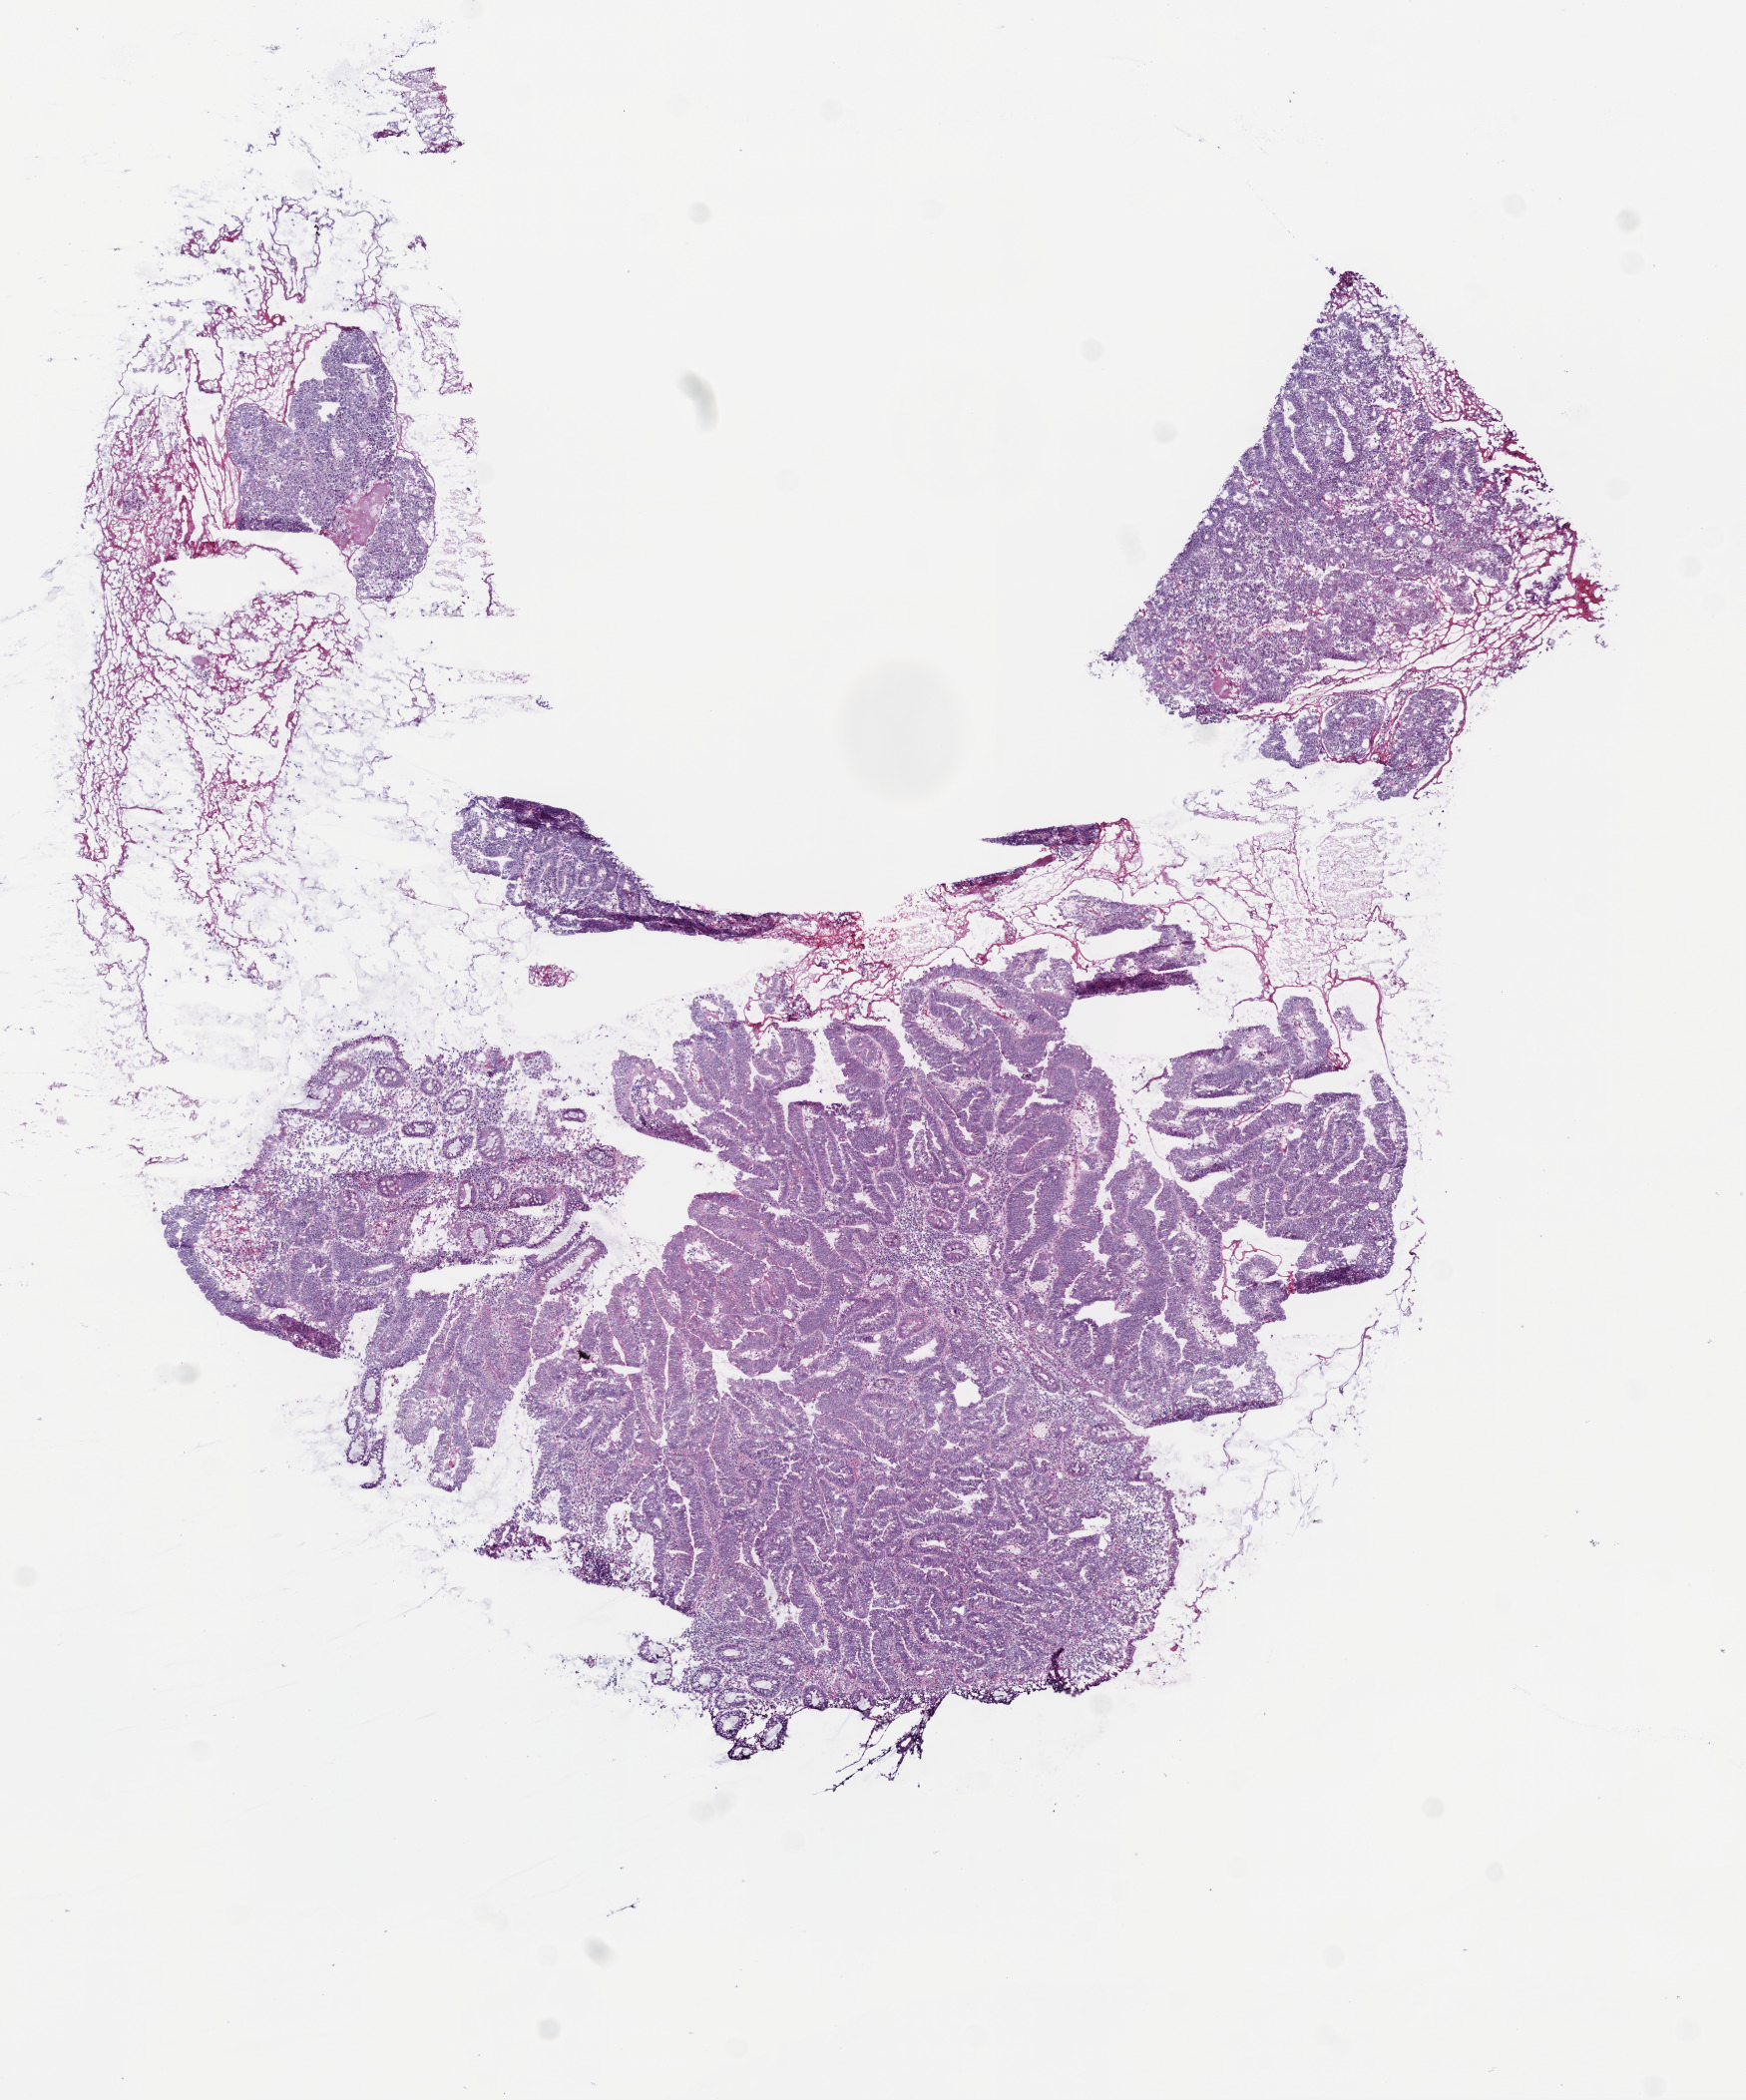
Whole-slide histology image, H&E-stained — shown as a low-resolution overview of the whole scanned area (about 7.0 x 8.4 mm); frozen section from the bottom of the tissue portion; rectum, primary tumour sample. Female patient; age at initial diagnosis 57 years. Composition of this section per pathologist review: tumour cells 87%, tumour nuclei 75%, normal cells 5%, stromal cells 5%, necrosis 3%.
AJCC pathologic stage: I (6th edition). Diagnosis: Adenocarcinoma, NOS. Lymph nodes positive (case pathology): 0 of 17 examined. TNM: T1 N0 M0.